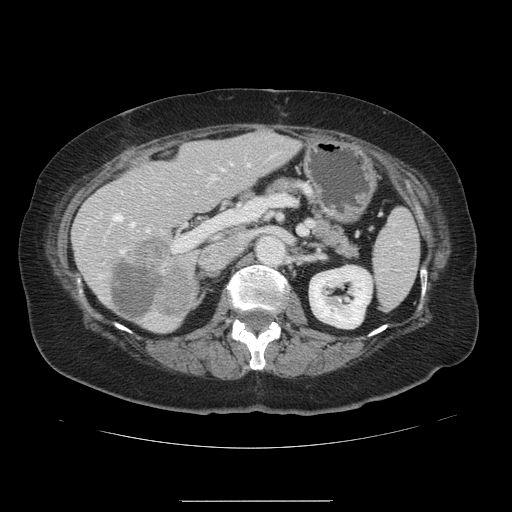
Contrast-enhanced abdominal CT, one axial slice; slice 66 of 141 in the series (ordered by position); 120 kVp; intravenous contrast given; soft-tissue window (W 400 / L 40 HU); 2.5 mm slice thickness; 512 × 512 image matrix, field of view 393 × 393 mm. Female patient, age 74 years. Case-level facts recorded for this patient, not image findings: diagnosis: colorectal cancer liver metastases, imaged before liver resection; multiple liver metastases: yes; largest metastasis: 7 cm; disease in both lobes: yes.
Structures marked on this image (outlined manually by an expert reader):
- hepatic veins: box from (x=113, y=183) to (x=158, y=231) px
- liver: (x=73, y=131)–(x=297, y=332)
- planned liver remnant (the part of the liver to remain after resection): (x=73, y=131)–(x=297, y=332)
- portal vein (with intrahepatic branches): (x=120, y=162)–(x=249, y=253)
- liver metastasis: (x=109, y=263)–(x=163, y=322)
- liver metastasis: (x=132, y=237)–(x=194, y=315)